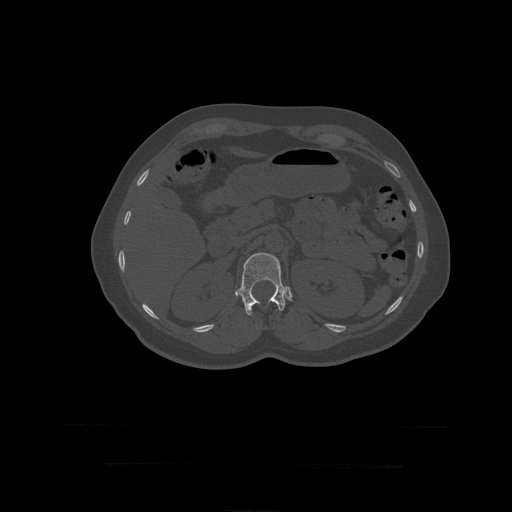
CT including the spine, one axial slice; slice 178 of 399 in the series (ordered by position); reconstruction kernel STANDARD; bone window (W 1800 / L 400 HU); 1.25 mm slice thickness; 512 × 512 image matrix, field of view 450 × 450 mm. Patient age 41 years. From the clinical record (not read from this slice): primary cancer: breast.
Annotated regions visible in this slice (semi-automatically segmented with operator editing):
- L1 vertebra: bounding box (x1, y1, x2, y2) in pixels: (238, 253, 287, 316)